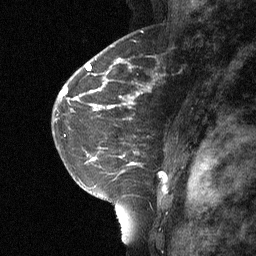
Breast MRI (dynamic contrast-enhanced), one sagittal slice. Slice 42 of 64 in the series (ordered by position). Dynamic contrast-enhanced study with each time point stored as its own series, time point 2 of 3 at this slice position (early post-contrast, ordered by acquisition time). 1.5 T. TE 4.8 ms, TR 27 ms. 256 × 256 image matrix, field of view 180 × 180 mm. Patient: female, 42 years. From the clinical record (not read from this slice): setting: breast cancer imaged before/during neoadjuvant chemotherapy; receptor status: triple-negative.
Structures marked on this image (semi-automatic segmentation, software-assisted and operator-edited):
- analysis volume of interest (the breast-tissue region the enhancement analysis was run in; not a lesion): box from (x=115, y=85) to (x=191, y=160) px
- tumour enhancement mask (voxels above the 90 % enhancement threshold inside the analysis volume of interest): (x=119, y=92)–(x=140, y=106)